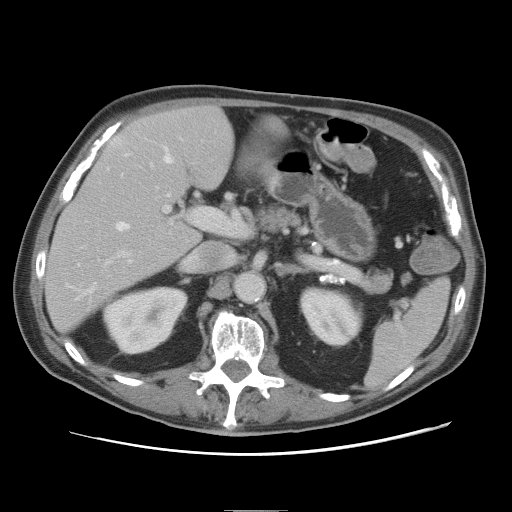
Contrast-enhanced abdominal CT, one axial slice. Position 42 of 89 along the scan axis. Intravenous contrast given. Soft-tissue window (W 400 / L 40 HU). 5 mm slice thickness. 512 × 512 image matrix, field of view 375 × 375 mm. Male patient, age 69 years. From the clinical record (not read from this slice): diagnosis: colorectal cancer liver metastases, imaged before liver resection; multiple liver metastases: no; largest metastasis: 8.5 cm; disease in both lobes: no.
Annotated regions visible in this slice (outlined manually by an expert reader):
- hepatic veins: bounding box (x1, y1, x2, y2) in pixels: (80, 147, 173, 297)
- liver: (45, 107, 277, 330)
- planned liver remnant (the part of the liver to remain after resection): (45, 107, 234, 329)
- portal vein (with intrahepatic branches): (108, 164, 224, 263)